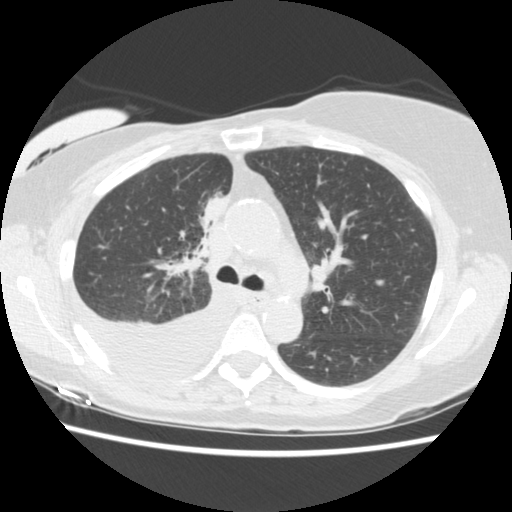
Low-dose screening chest CT, one axial slice. Position 99 of 157 along the scan axis. Reconstruction kernel STANDARD. Lung window (W 1500 / L -600 HU). 2.5 mm slice thickness. 512 × 512 image matrix, field of view 330 × 330 mm.
Outlined on this slice (expert manual segmentation):
- lesion 1 (tumor, upper lobe of right lung): bounding box [x1, y1, x2, y2] px = [203, 197, 227, 229]